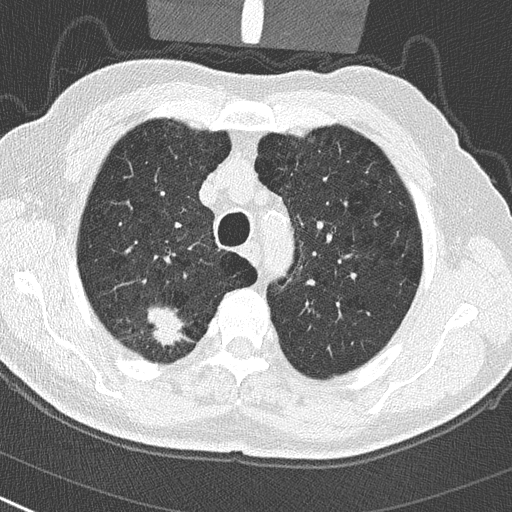
Low-dose screening chest CT, one axial slice. Position 227 of 290 along the scan axis. Reconstruction kernel B50f. Lung window (W 1500 / L -600 HU). 512 × 512 image matrix, field of view 300 × 300 mm.
Annotated regions visible in this slice (manually delineated by an expert):
- lesion 1 (tumor, upper lobe of right lung): bounding box [x1, y1, x2, y2] px = [147, 306, 188, 348]